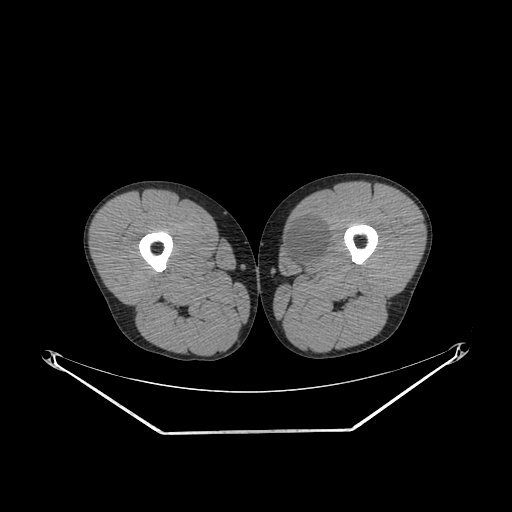
CT of an extremity soft-tissue mass (from a PET/CT study), one axial slice; slice 252 of 311 in the series (ordered by position); reconstruction kernel SOFT; 140 kVp; soft-tissue window (W 400 / L 40 HU); 512 × 512 image matrix. Male patient. From the clinical record (not read from this slice): histological type: mixoid liposarcoma; grade: low; site of the primary tumour: left thigh.
Annotated regions visible in this slice (expert contour drawn on MRI and transferred to this co-registered scan by the dataset authors):
- gross tumour volume (mass): bounding box <283,217,328,264> (left, top, right, bottom; pixels)